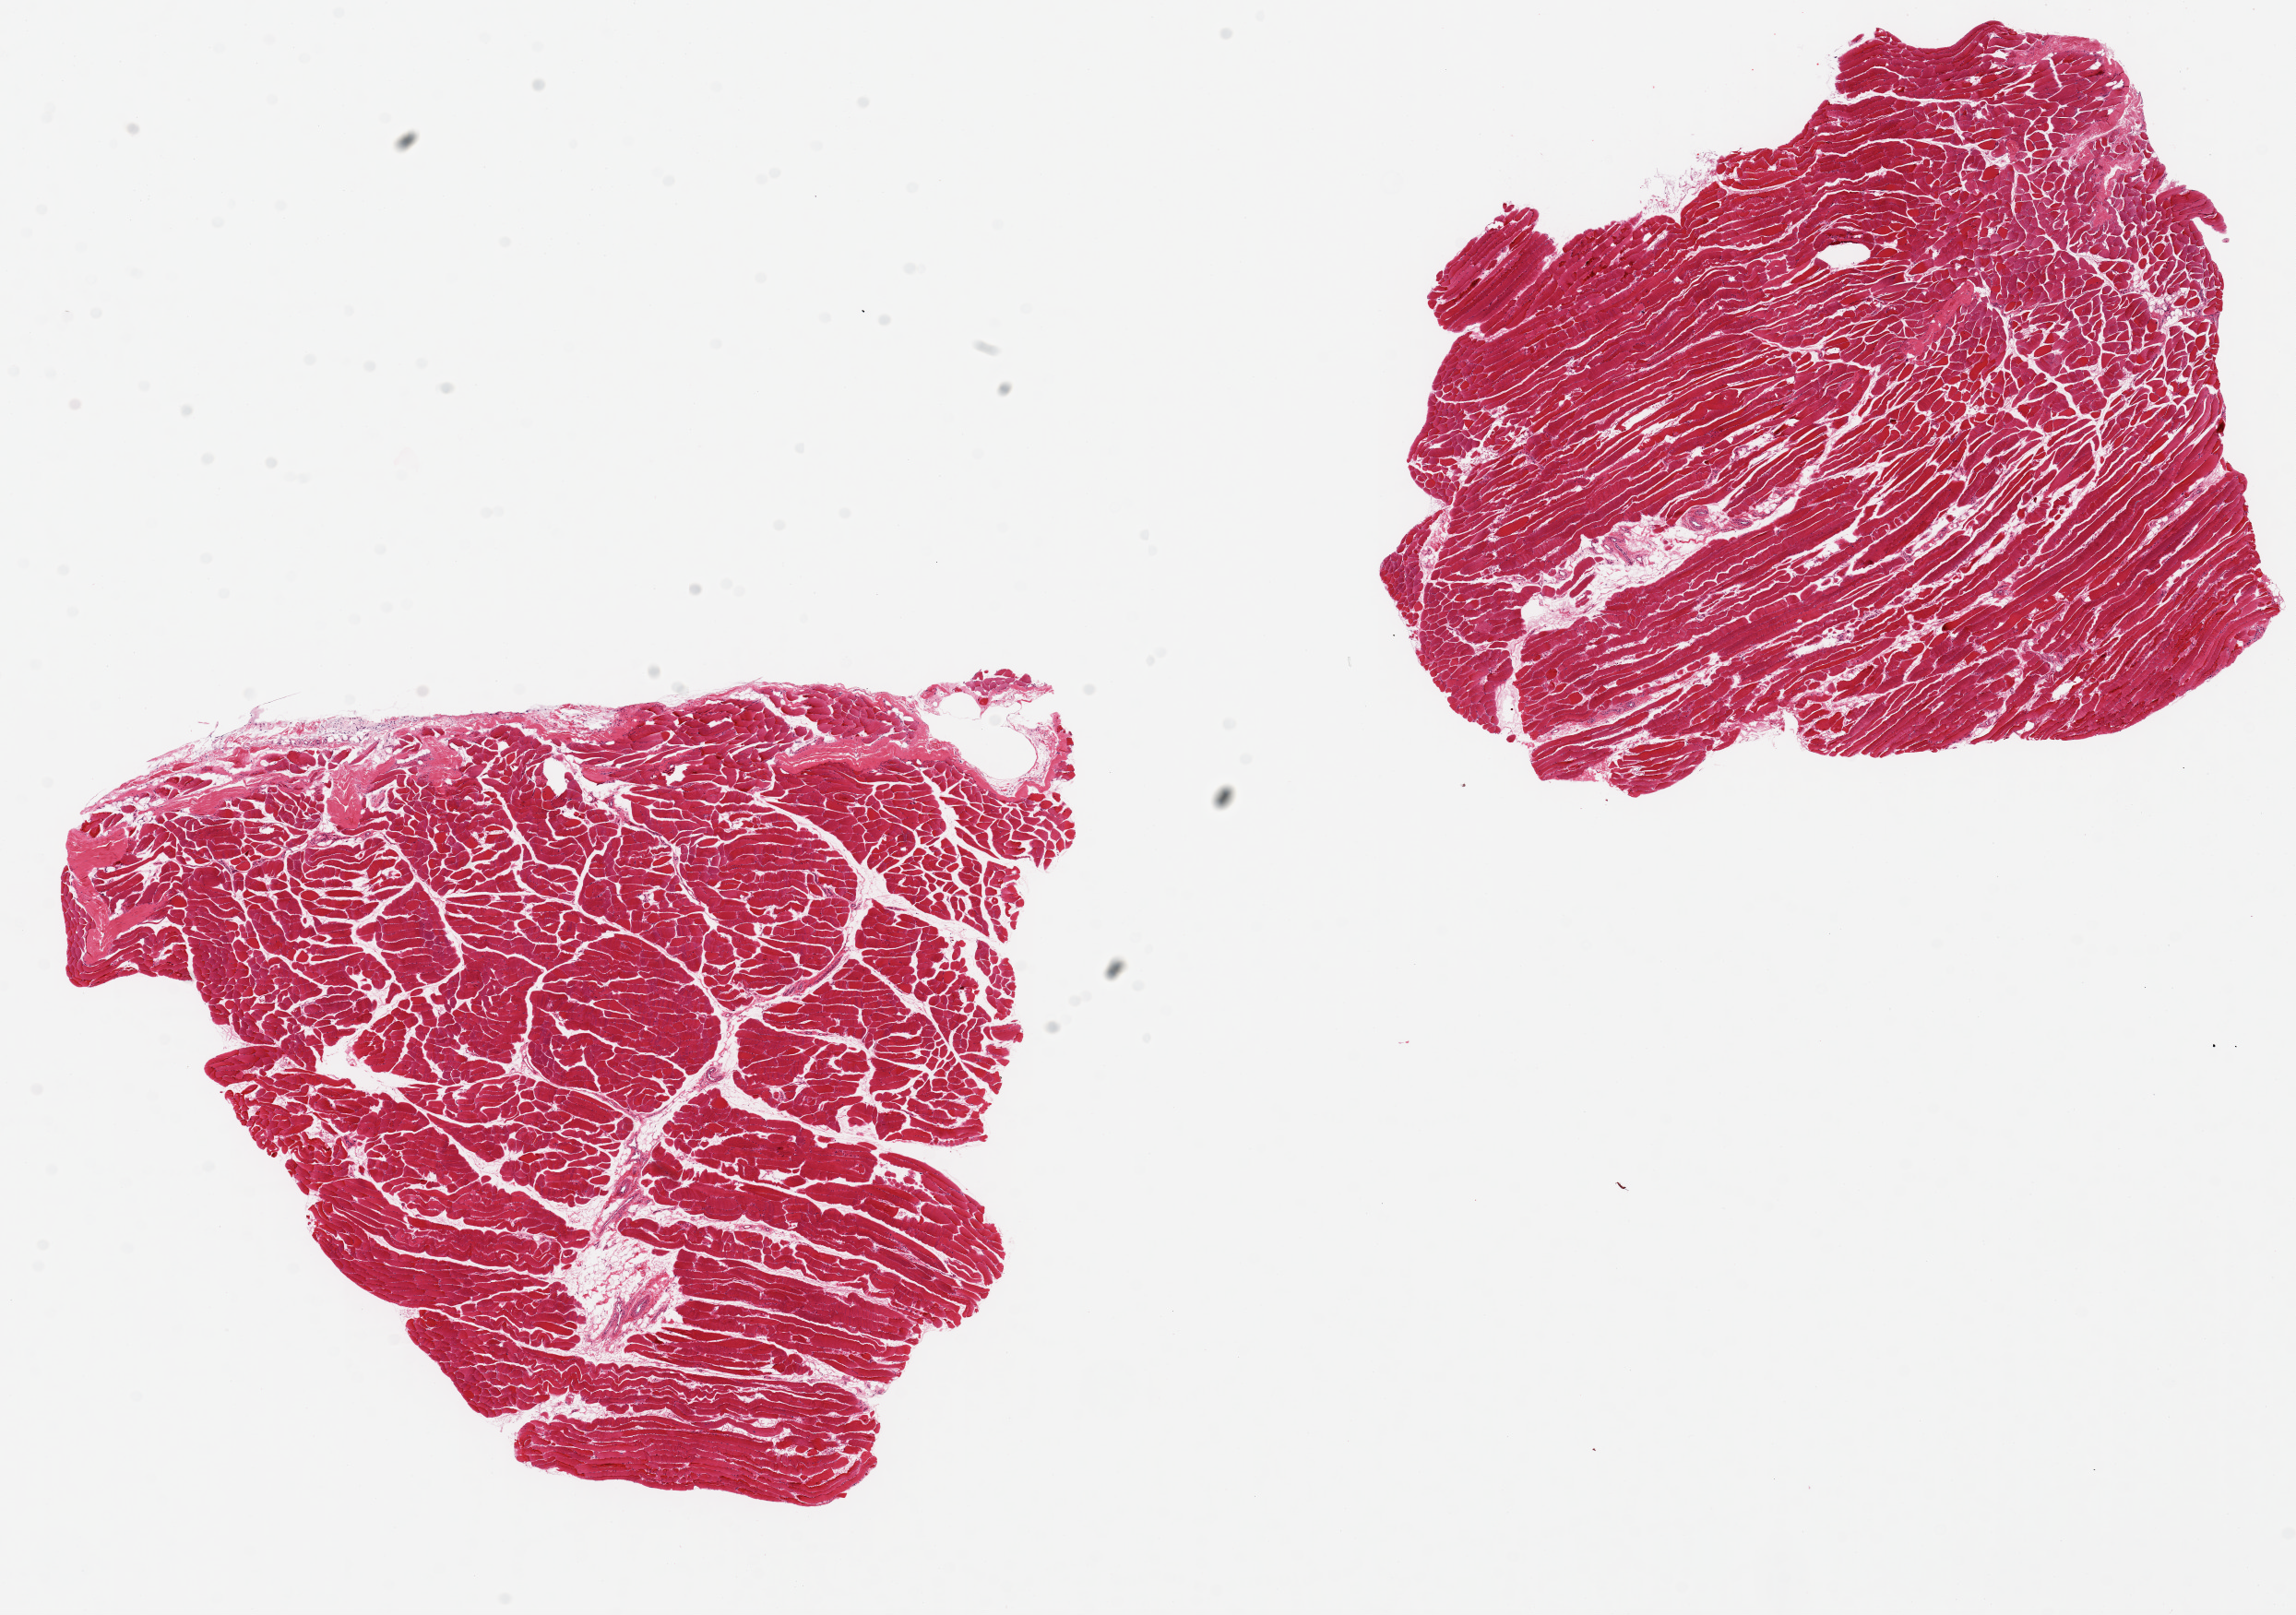
Whole-slide image, H&E stain, shown as a low-resolution overview of the whole scanned area (about 19.7 x 13.9 mm). PAXgene-fixed paraffin-embedded (PFPE) section. Sampled site (target tissue): skeletal muscle. Tissue donor sample.
Review note (as recorded): 2 pieces, 9x7 & 8x6mm; <5% internal adipose.